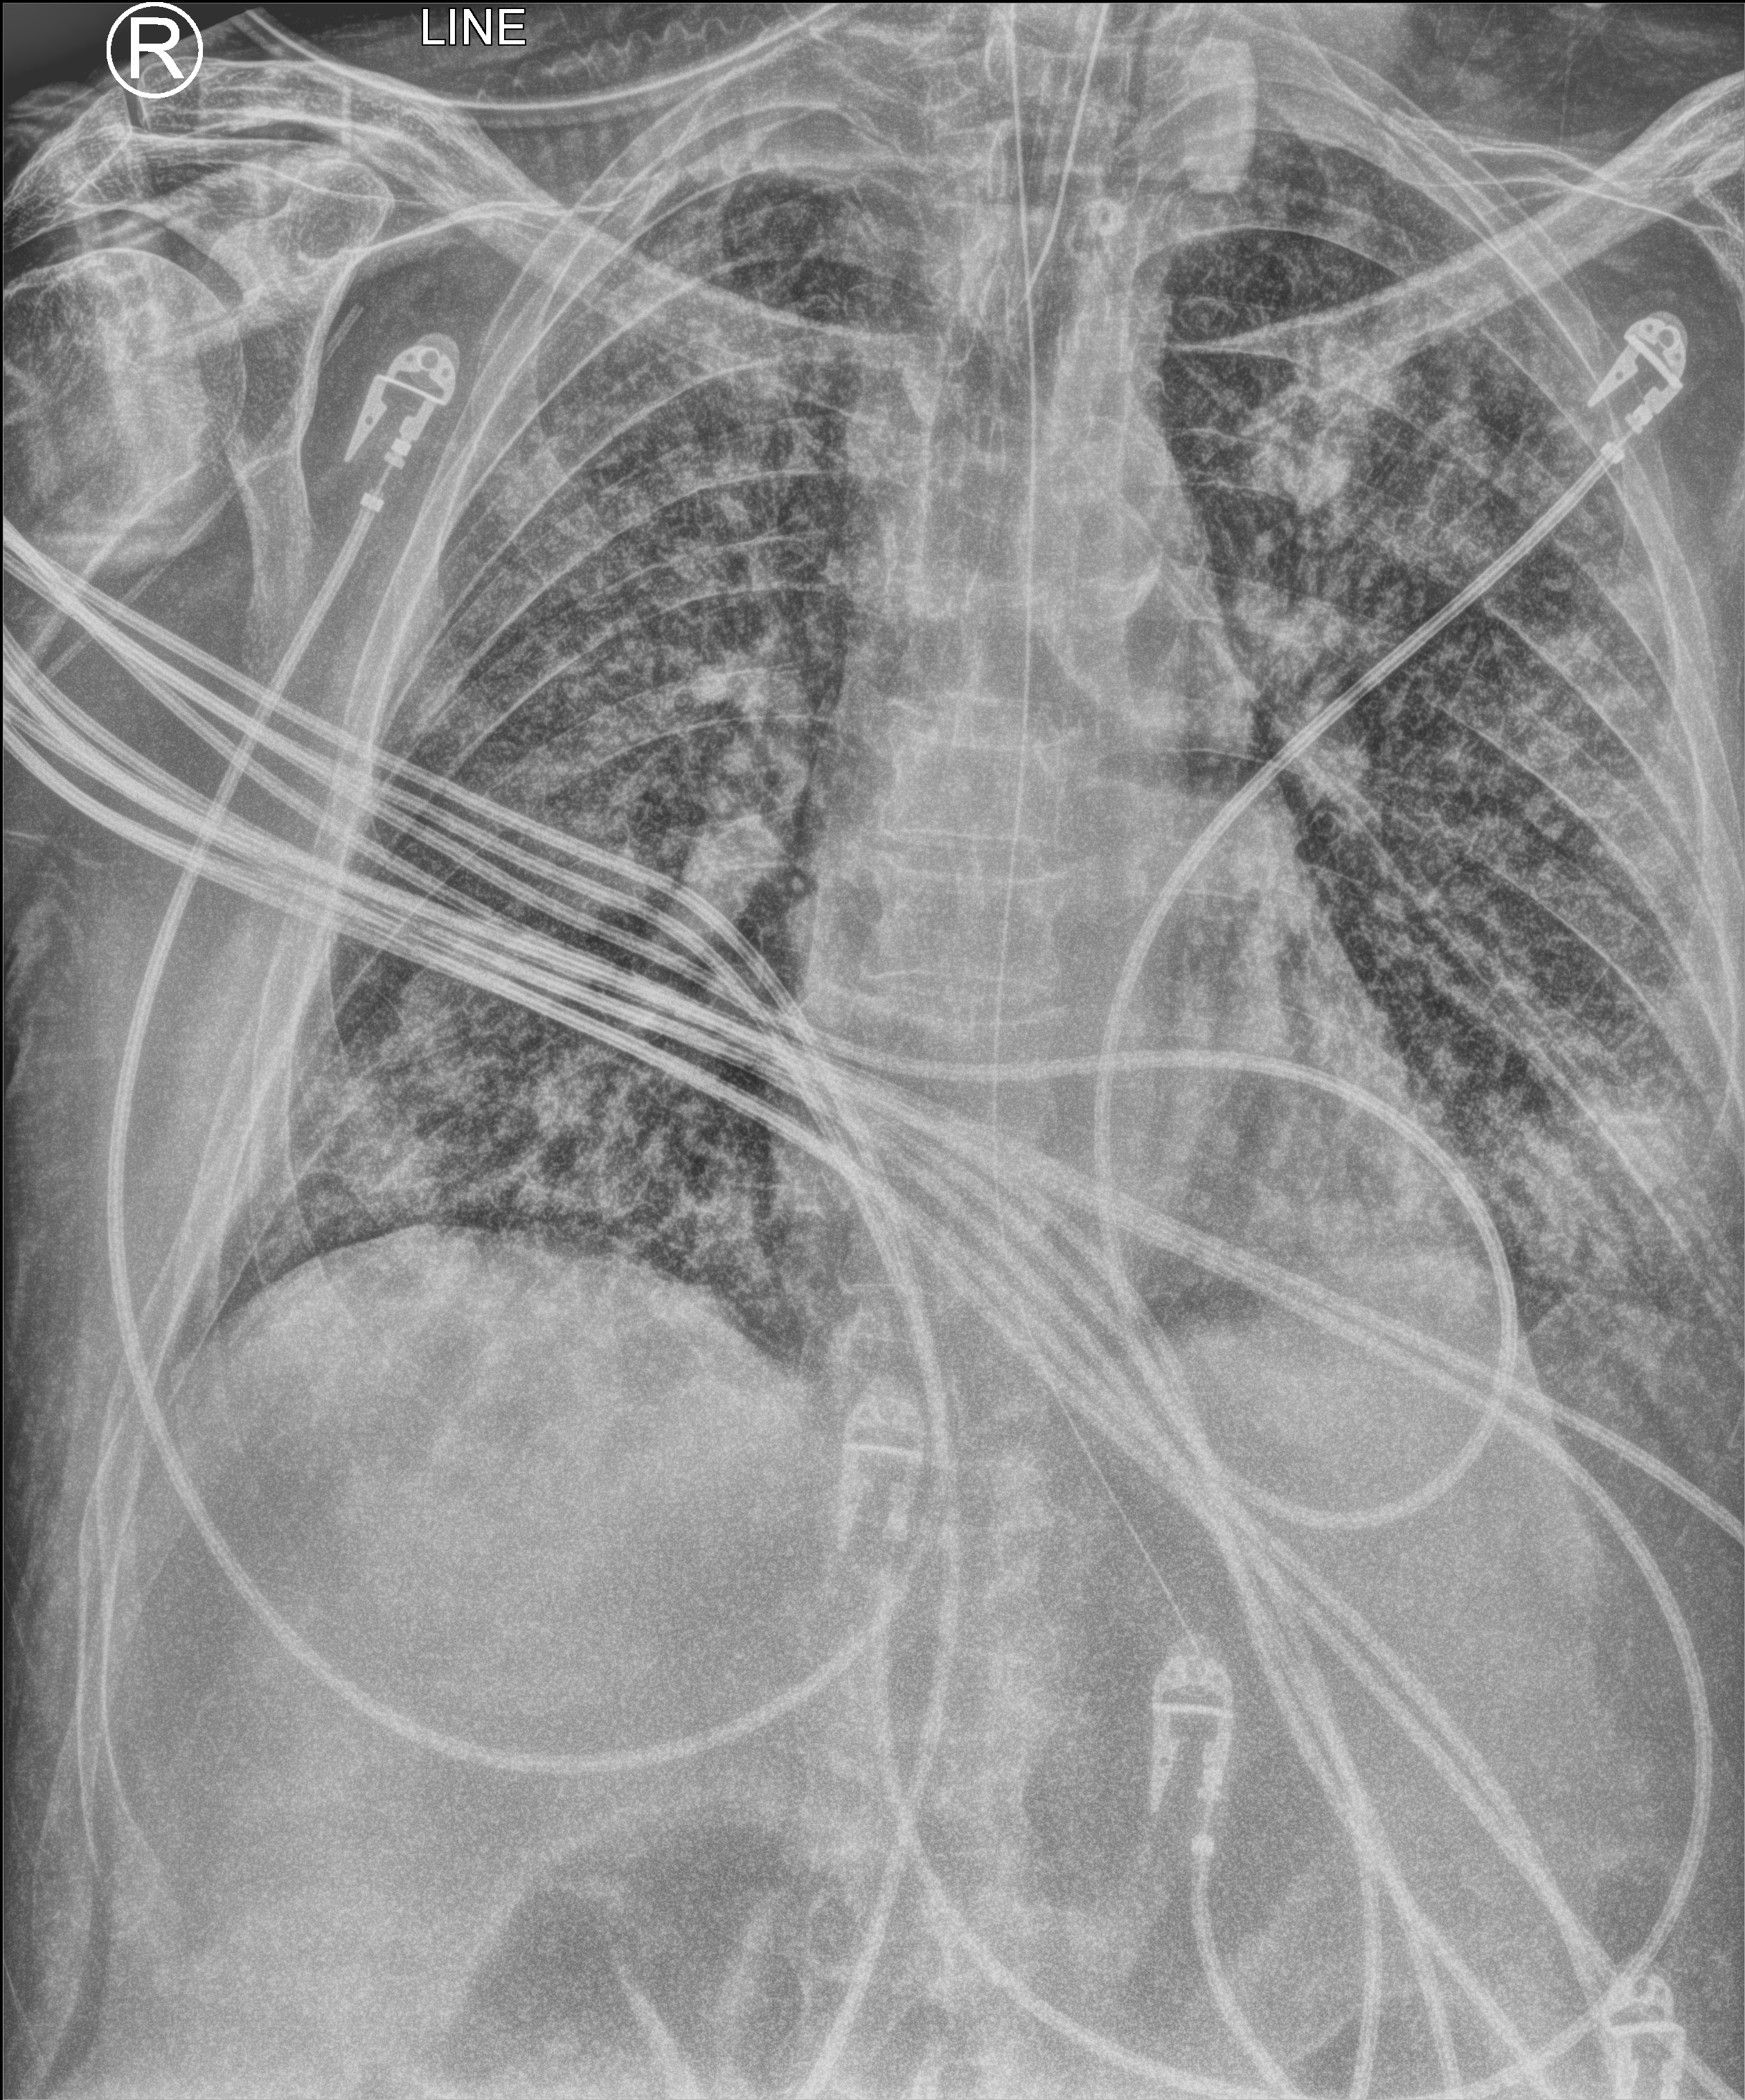
Chest X-ray (portable). Male patient hospitalised with COVID-19, age 60–74 years.
Hospital-stay facts (about this admission, not read from this image; timing relative to this image not recorded): admitted to intensive care during this hospital stay: yes.